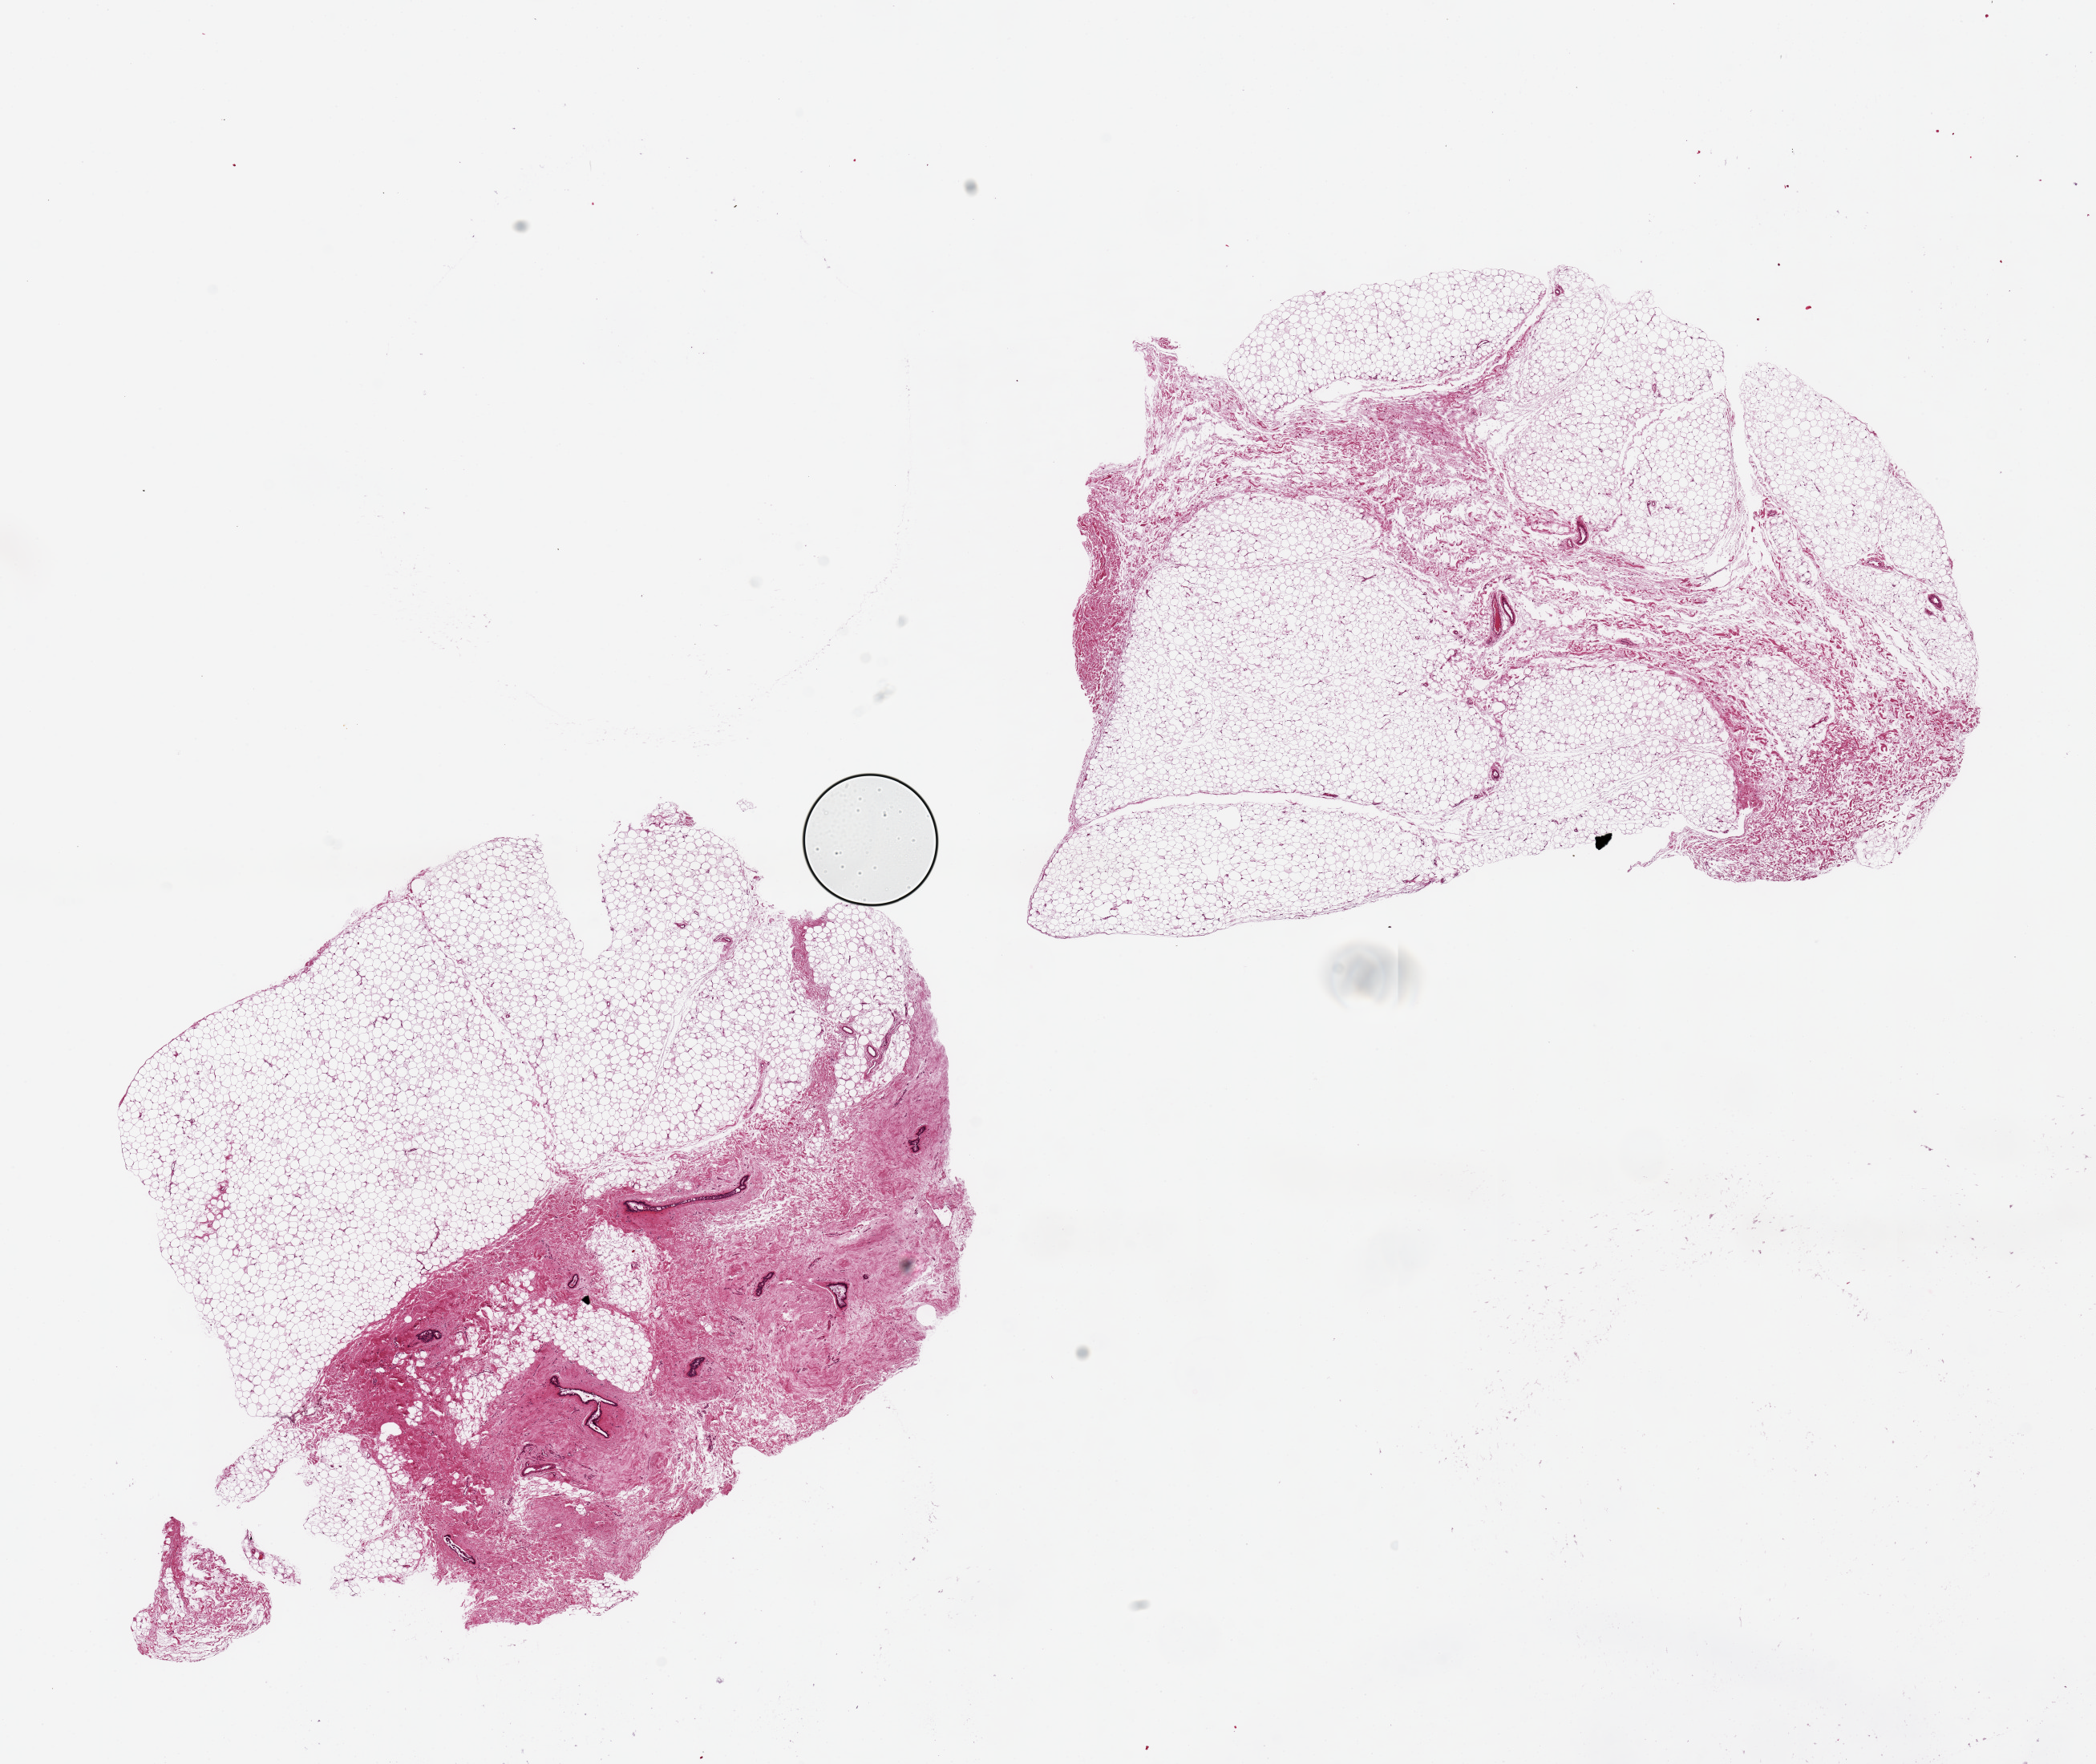
H&E whole-slide image — whole scanned area (about 20.7 x 17.4 mm) shown as a low-resolution overview, PAXgene-fixed paraffin-embedded (PFPE) section, sampled site (target tissue): breast, donor tissue sample. Male donor.
* review note (as recorded): 2 pieces, 10x7 & 10x6mm; ducts present